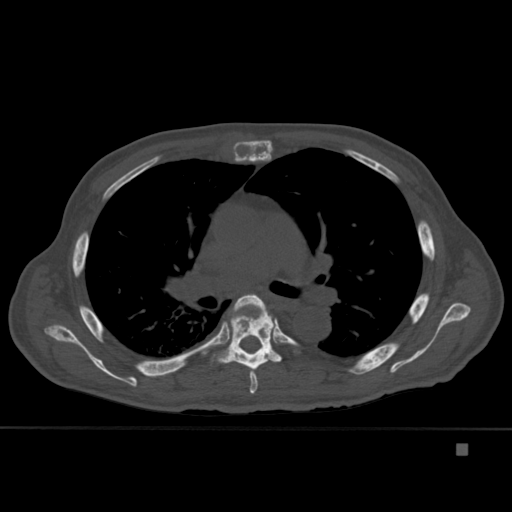
CT including the spine, one axial slice; position 296 of 451 along the scan axis; bone window (W 1800 / L 400 HU); 1.5 mm slice thickness; 512 × 512 image matrix, field of view 378 × 378 mm. Patient: male, 75 years. Case-level facts recorded for this patient, not image findings: primary cancer: prostate.
Outlined on this slice (semi-automatically segmented with operator editing):
- T5 vertebra: bounding box (x1, y1, x2, y2) in pixels: (232, 294, 266, 394)
- T6 vertebra: (212, 307, 282, 370)